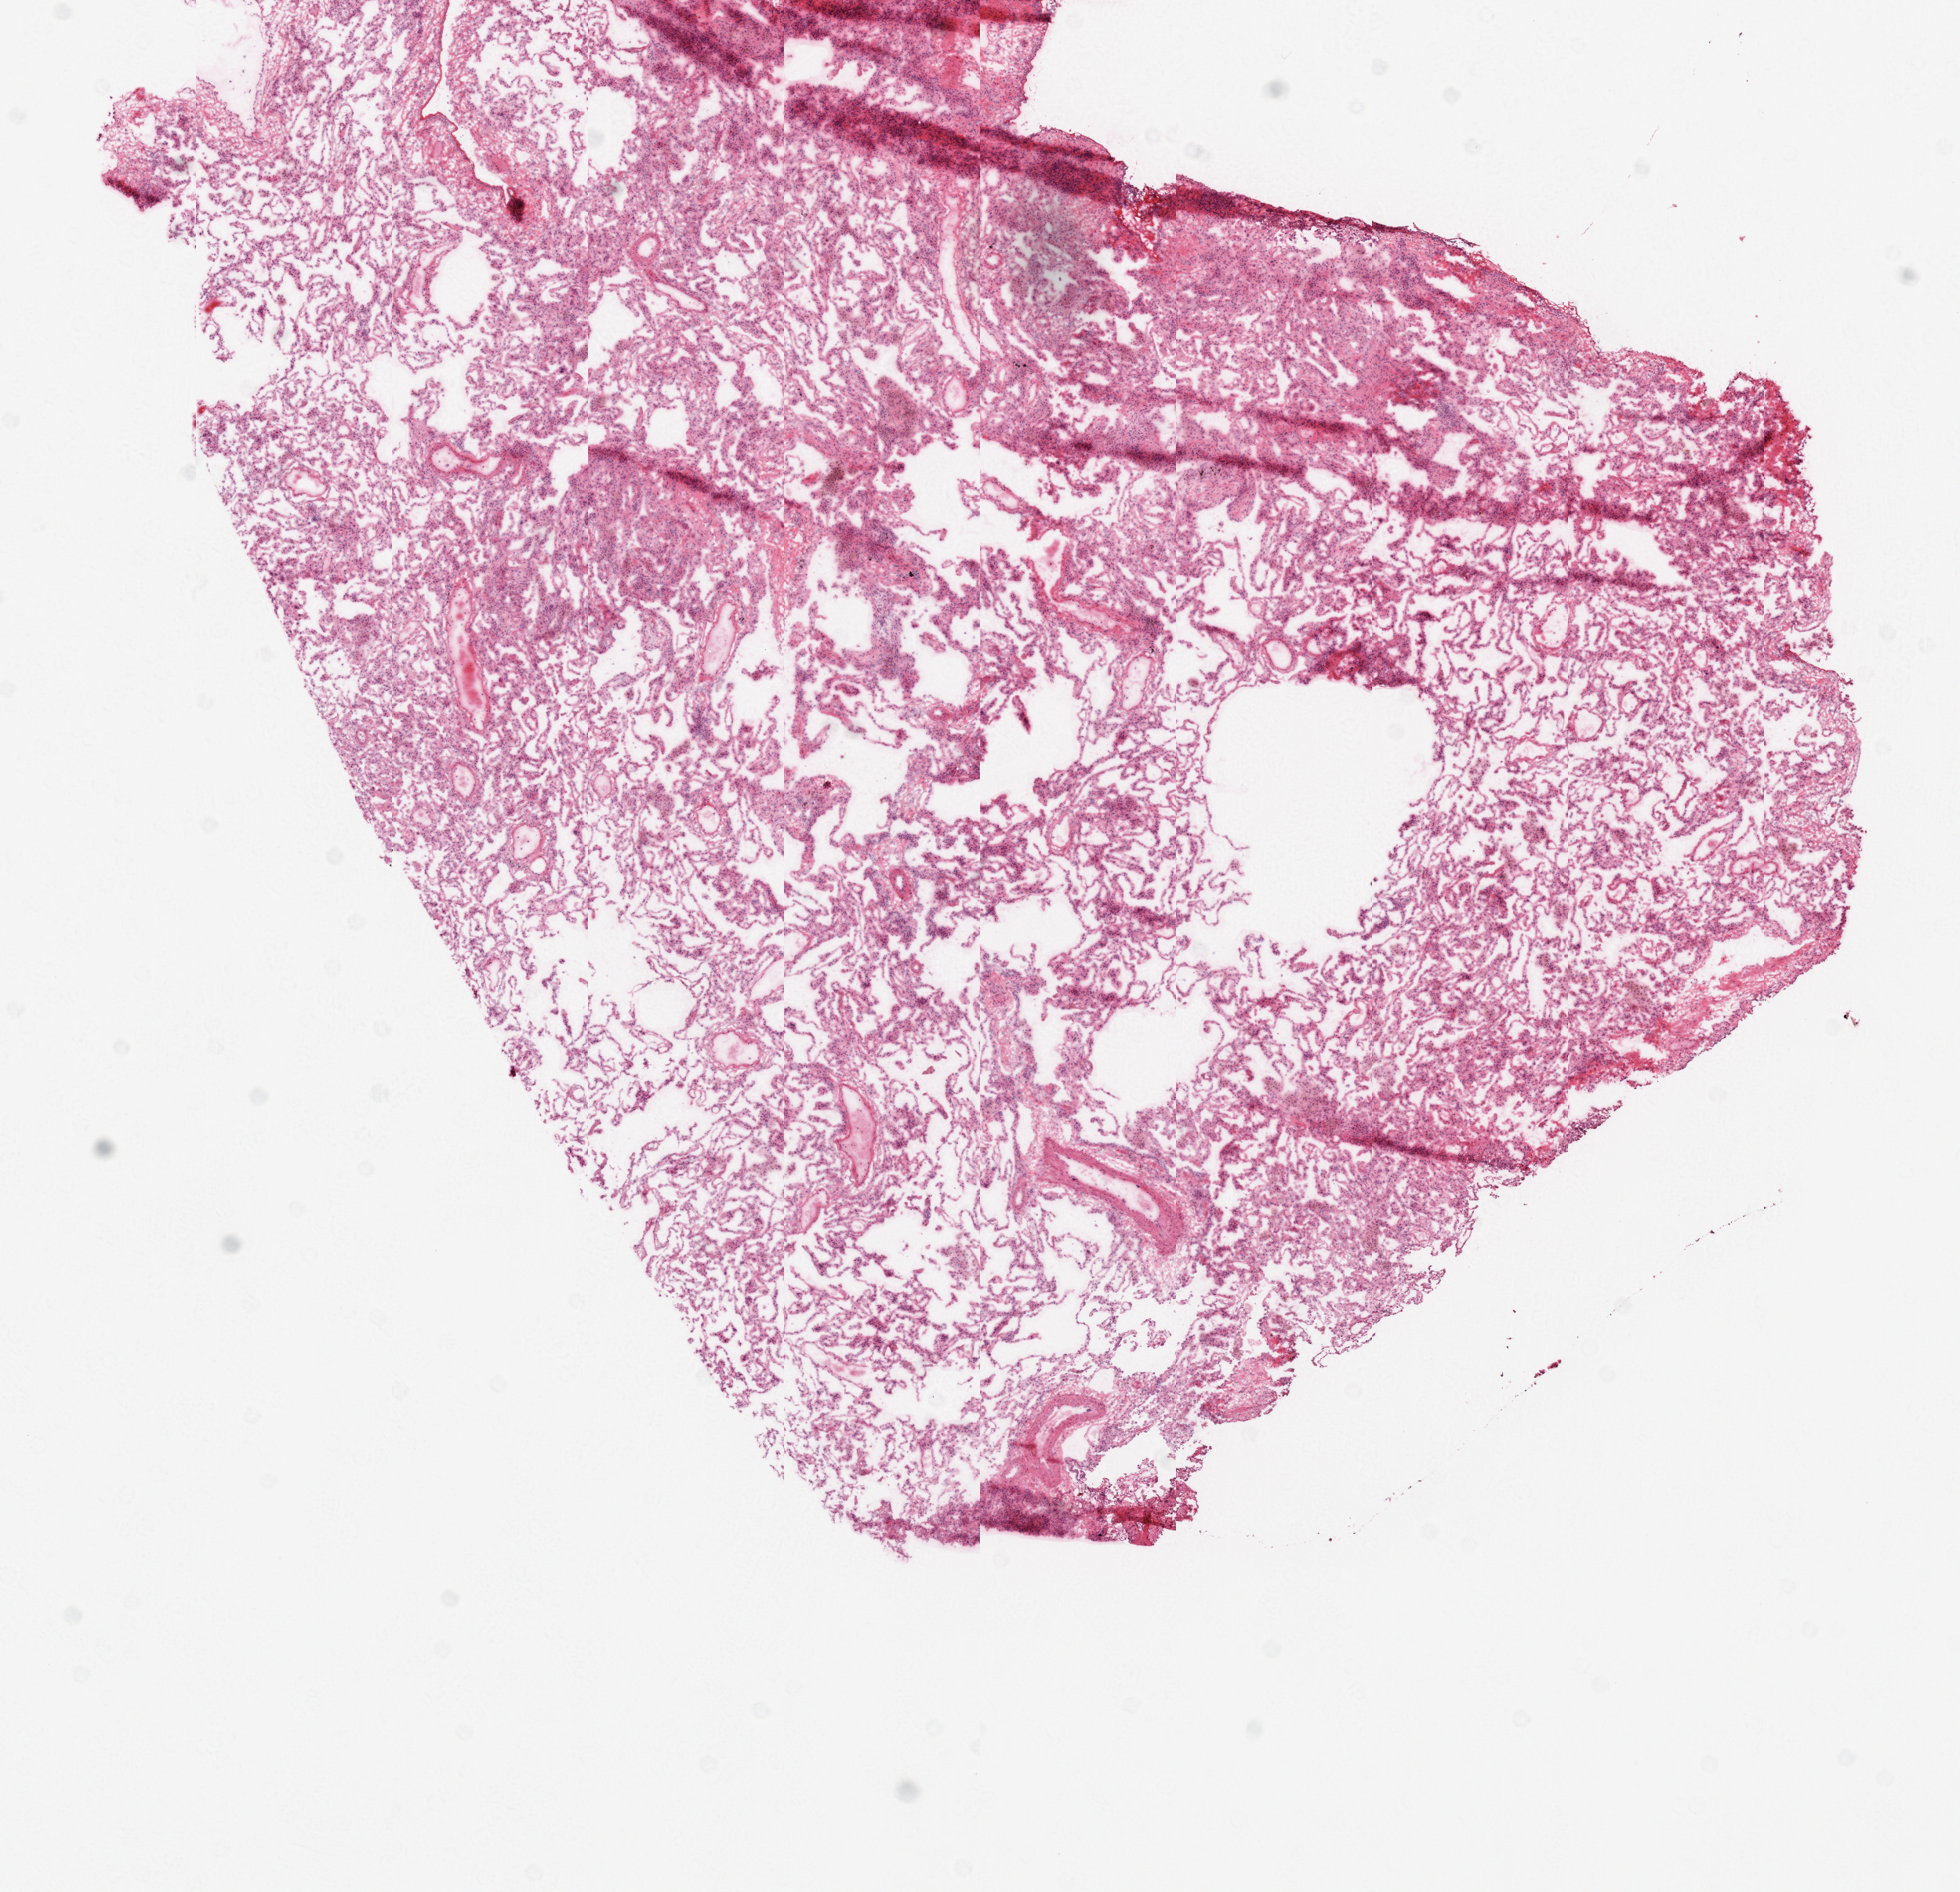
Whole-slide histology image, H&E-stained — a low-resolution overview of the entire scanned area, about 10.0 x 9.7 mm (acquisition: 20x scan); frozen section from the top of the tissue portion; sample: solid tissue normal (non-tumour tissue), lung. Patient: male, age at initial diagnosis 77 years.
This section: solid tissue normal sample (biorepository sample class). Patient diagnosis: Squamous cell carcinoma, NOS (lower lobe, lung).